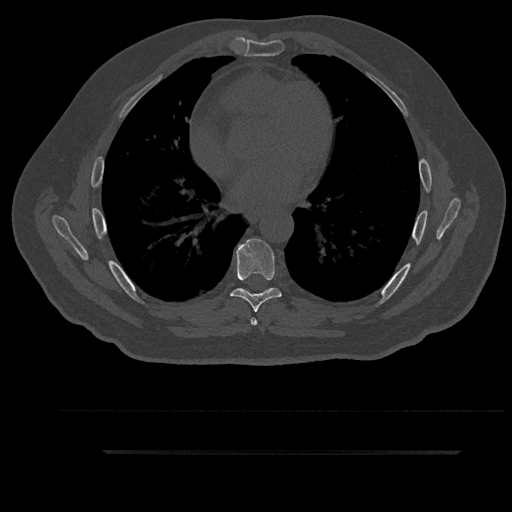
CT including the spine, one axial slice; position 526 of 797 along the scan axis; bone window (W 1800 / L 400 HU); 0.5 mm slice thickness; 512 × 512 image matrix. Male patient, age 63 years. From the clinical record (not read from this slice): primary cancer: renal; vertebrae with lytic lesions (as recorded): T8.
Structures marked on this image (semi-automatically segmented with operator editing):
- T6 vertebra: bounding box (x1, y1, x2, y2) in pixels: (251, 291, 265, 326)
- T7 vertebra: (230, 239, 281, 312)